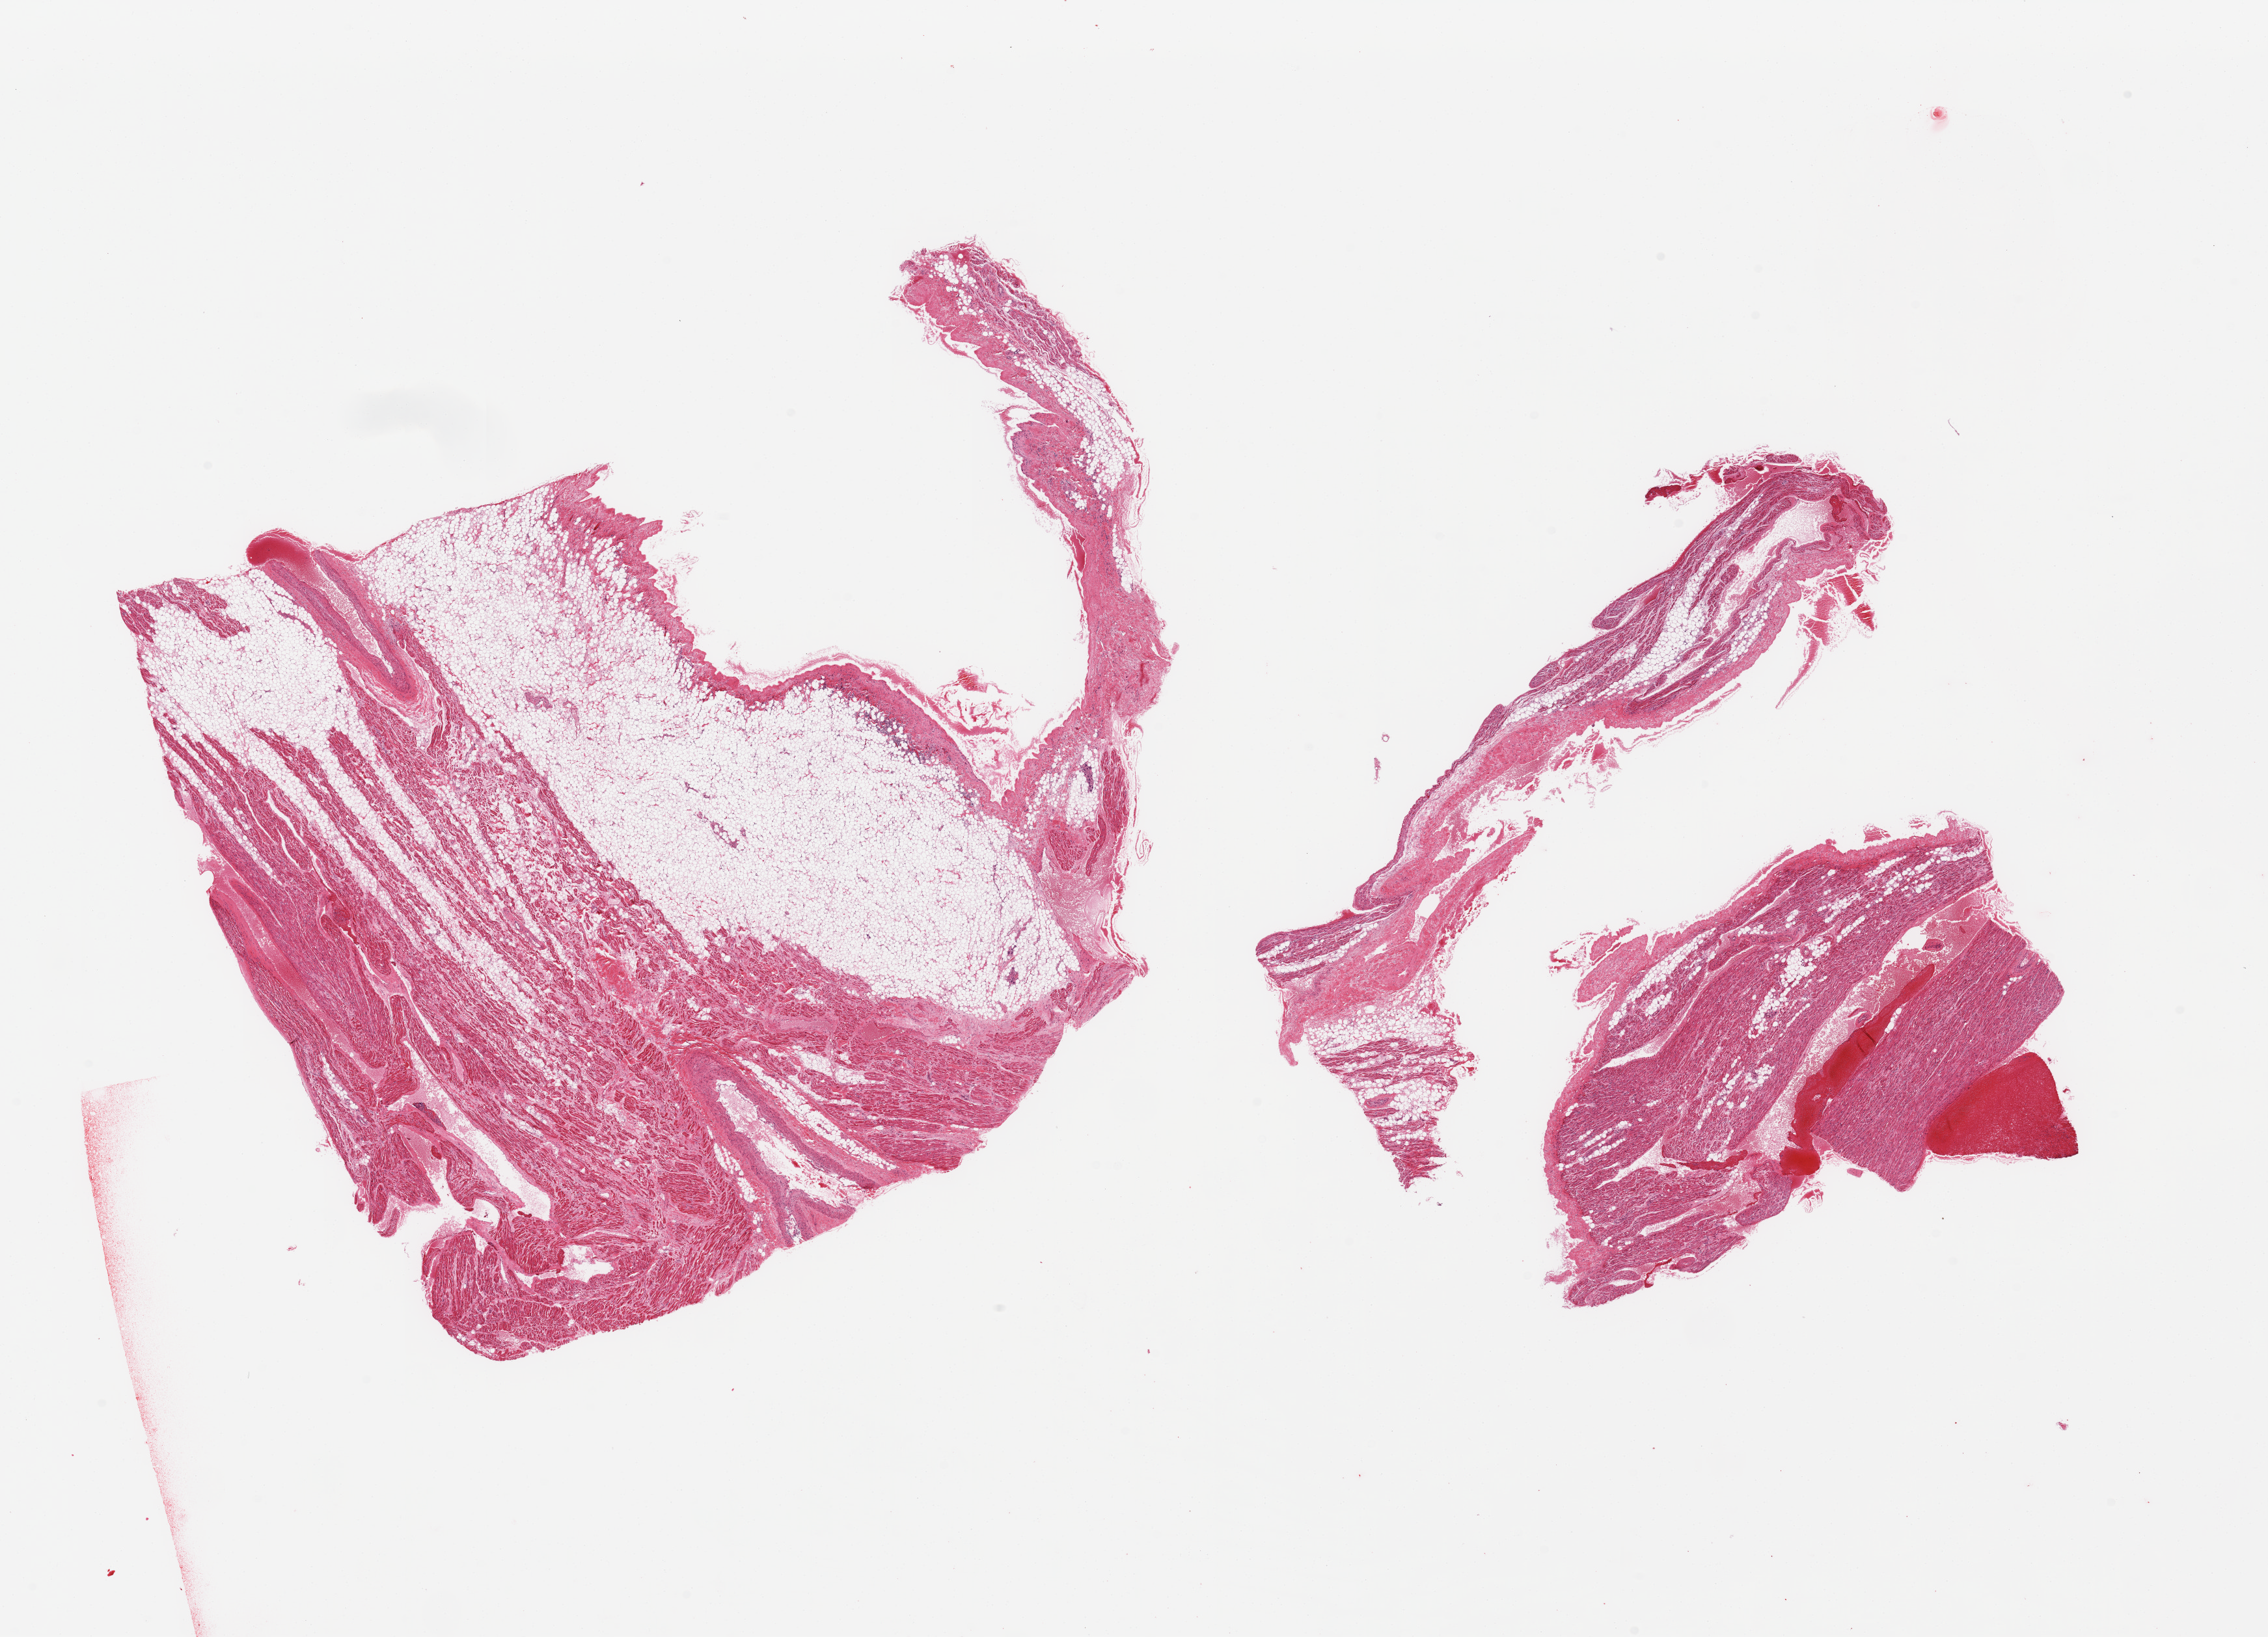
H&E whole-slide image — low-resolution overview of the scanned area, about 27.6 x 19.9 mm (from a 20x scan), PAXgene-fixed, paraffin-embedded tissue, section of auricular appendage (target tissue), donor tissue sample.
Review note (as recorded): 2 pieces, no abnormalities.